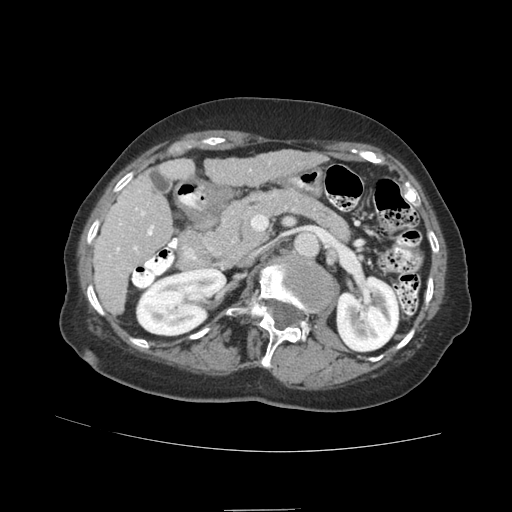
Contrast-enhanced abdominal CT (liver protocol), one axial slice. Position 37 of 89 along the scan axis. Reconstruction kernel STANDARD. 140 kVp. Soft-tissue window (W 400 / L 40 HU). 2.5 mm slice thickness. 512 × 512 image matrix. Case-level facts recorded for this patient, not image findings: diagnosis: hepatocellular carcinoma (patient treated with transarterial chemoembolisation; whether this scan precedes or follows treatment is not stated here); TNM stage (as recorded): Stage-II; Child-Pugh class: A; tumour nodularity: multinodular; tumour size: 4 cm.
Annotated regions visible in this slice (semi-automatic segmentation, software-assisted and operator-edited):
- liver parenchyma outside the tumour (the mass and vessels are separate outlines, so this box may not span the whole liver): bounding box (x1, y1, x2, y2) in pixels: (93, 150, 324, 314)
- liver vessels: (116, 169, 251, 253)